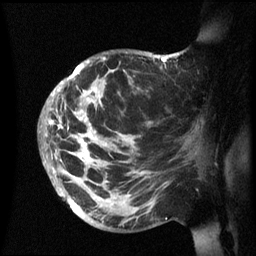
Breast MRI (dynamic contrast-enhanced), one sagittal slice. Position 40 of 60 along the scan axis. Dynamic contrast-enhanced series, image 2 of 3 at this slice position (ordered by acquisition). 1.5 T. TE 4.2 ms, TR 8.4 ms. 2.4 mm slice thickness. 256 × 256 image matrix, field of view 230 × 230 mm. Female patient, age 48 years.
Outlined on this slice (semi-automatic segmentation, software-assisted and operator-edited):
- analysis volume of interest (the breast-tissue region the enhancement analysis was run in; not a lesion): bounding box (x1, y1, x2, y2) in pixels: (42, 51, 202, 236)
- tumour enhancement mask (voxels above the 70 % enhancement threshold inside the analysis volume of interest): (44, 54, 178, 204)